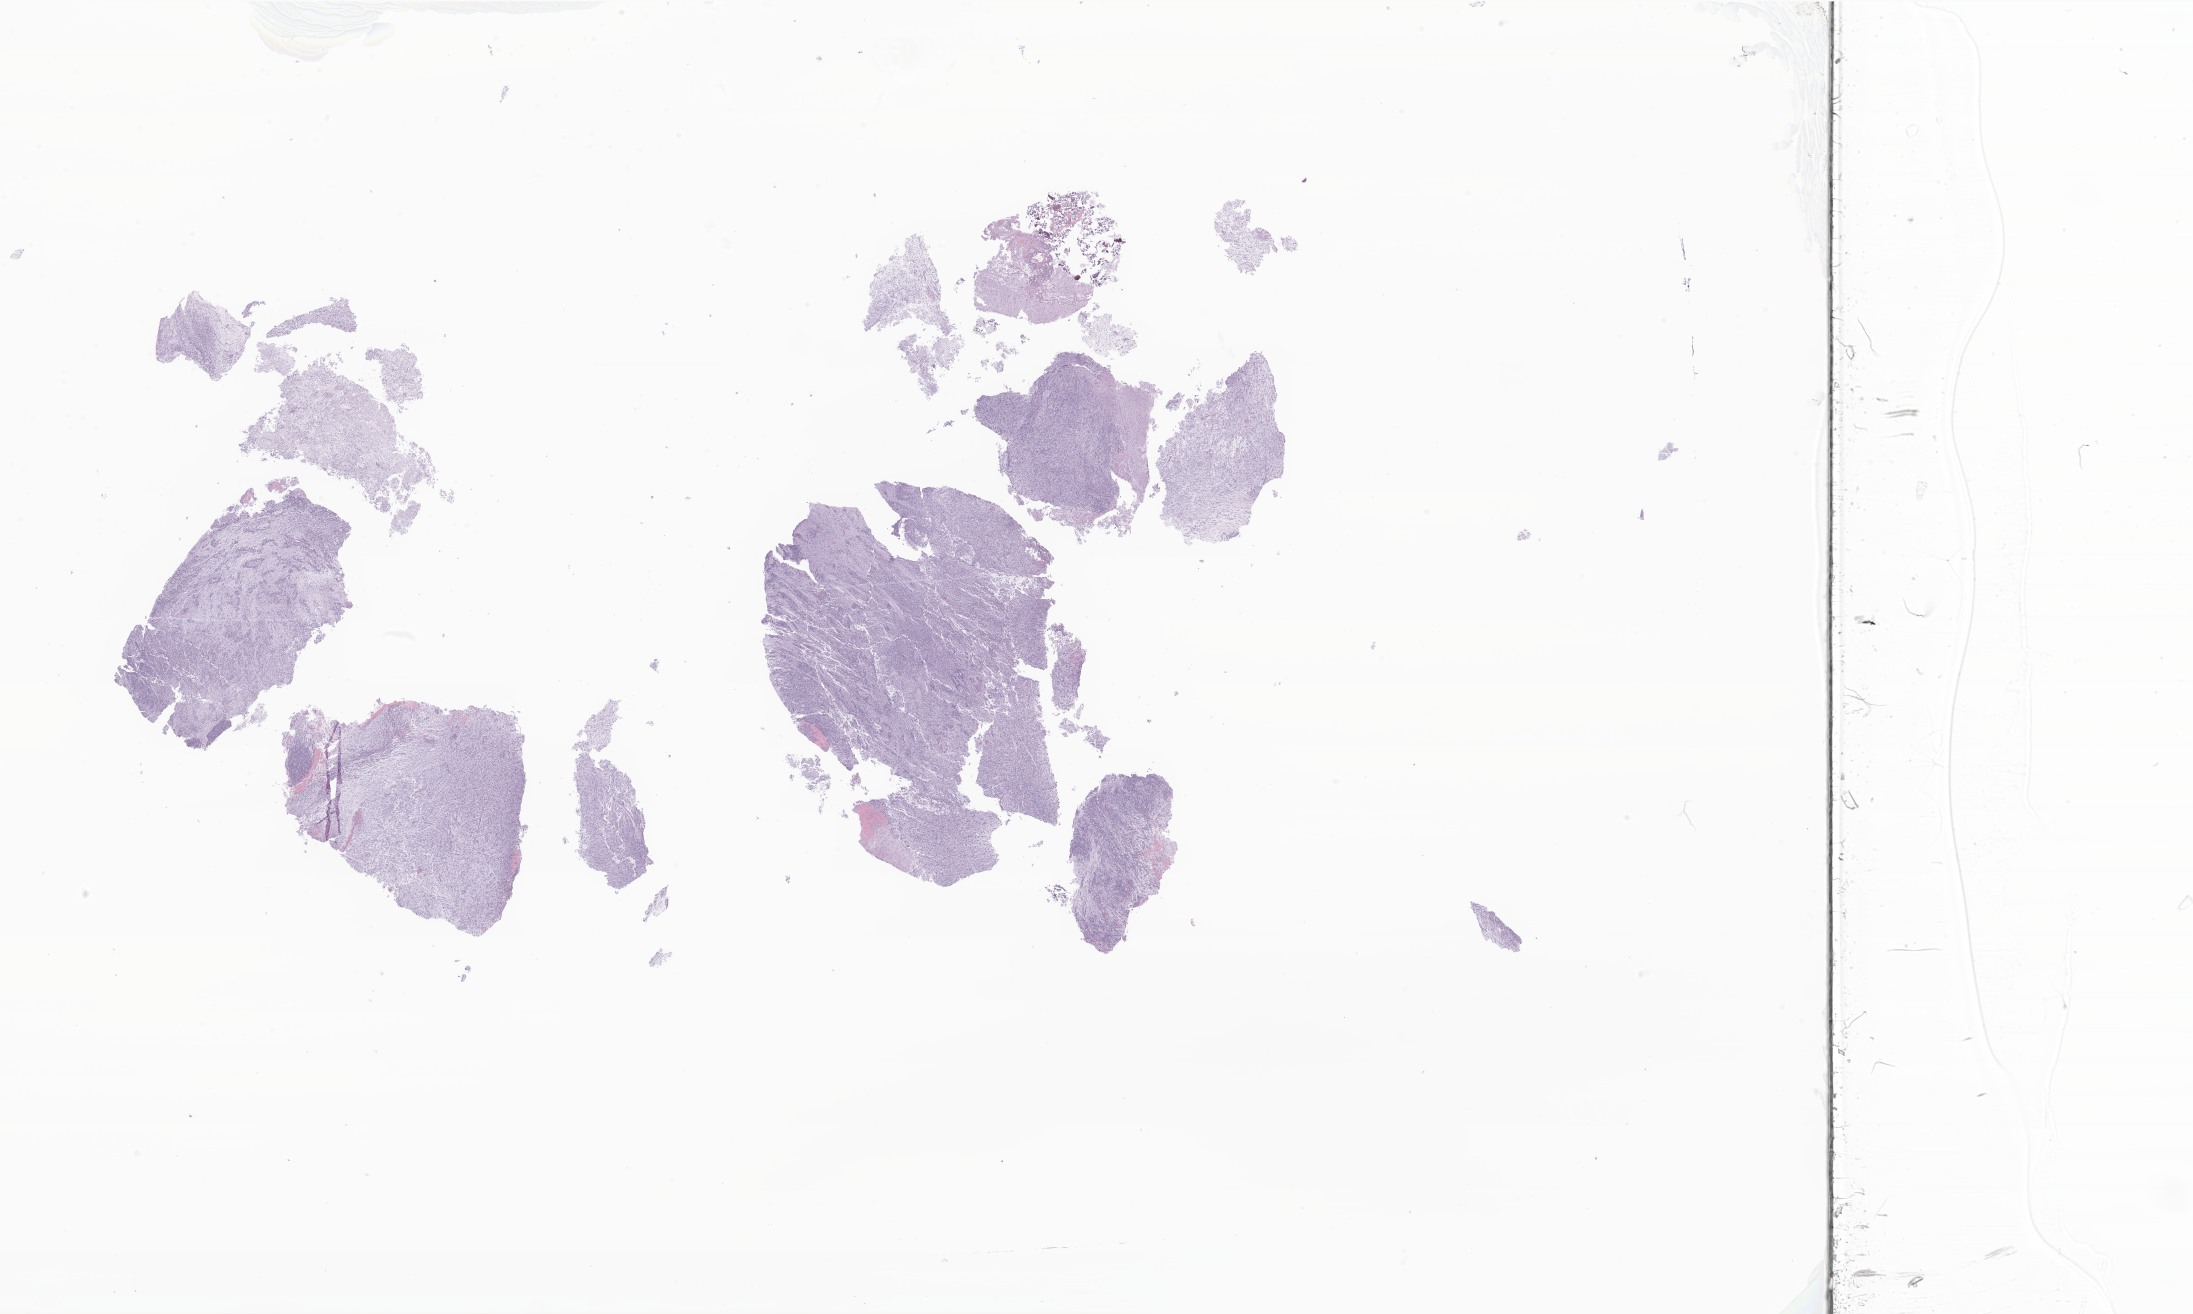
Whole-slide image, hematoxylin and eosin (H&E) stain of tumor tissue from the brain, whole scanned area (about 36.9 x 22.1 mm) shown as a low-resolution overview; formalin-fixed paraffin-embedded section. Female patient, age 798 days.
Diagnosis: Glioma, malignant.